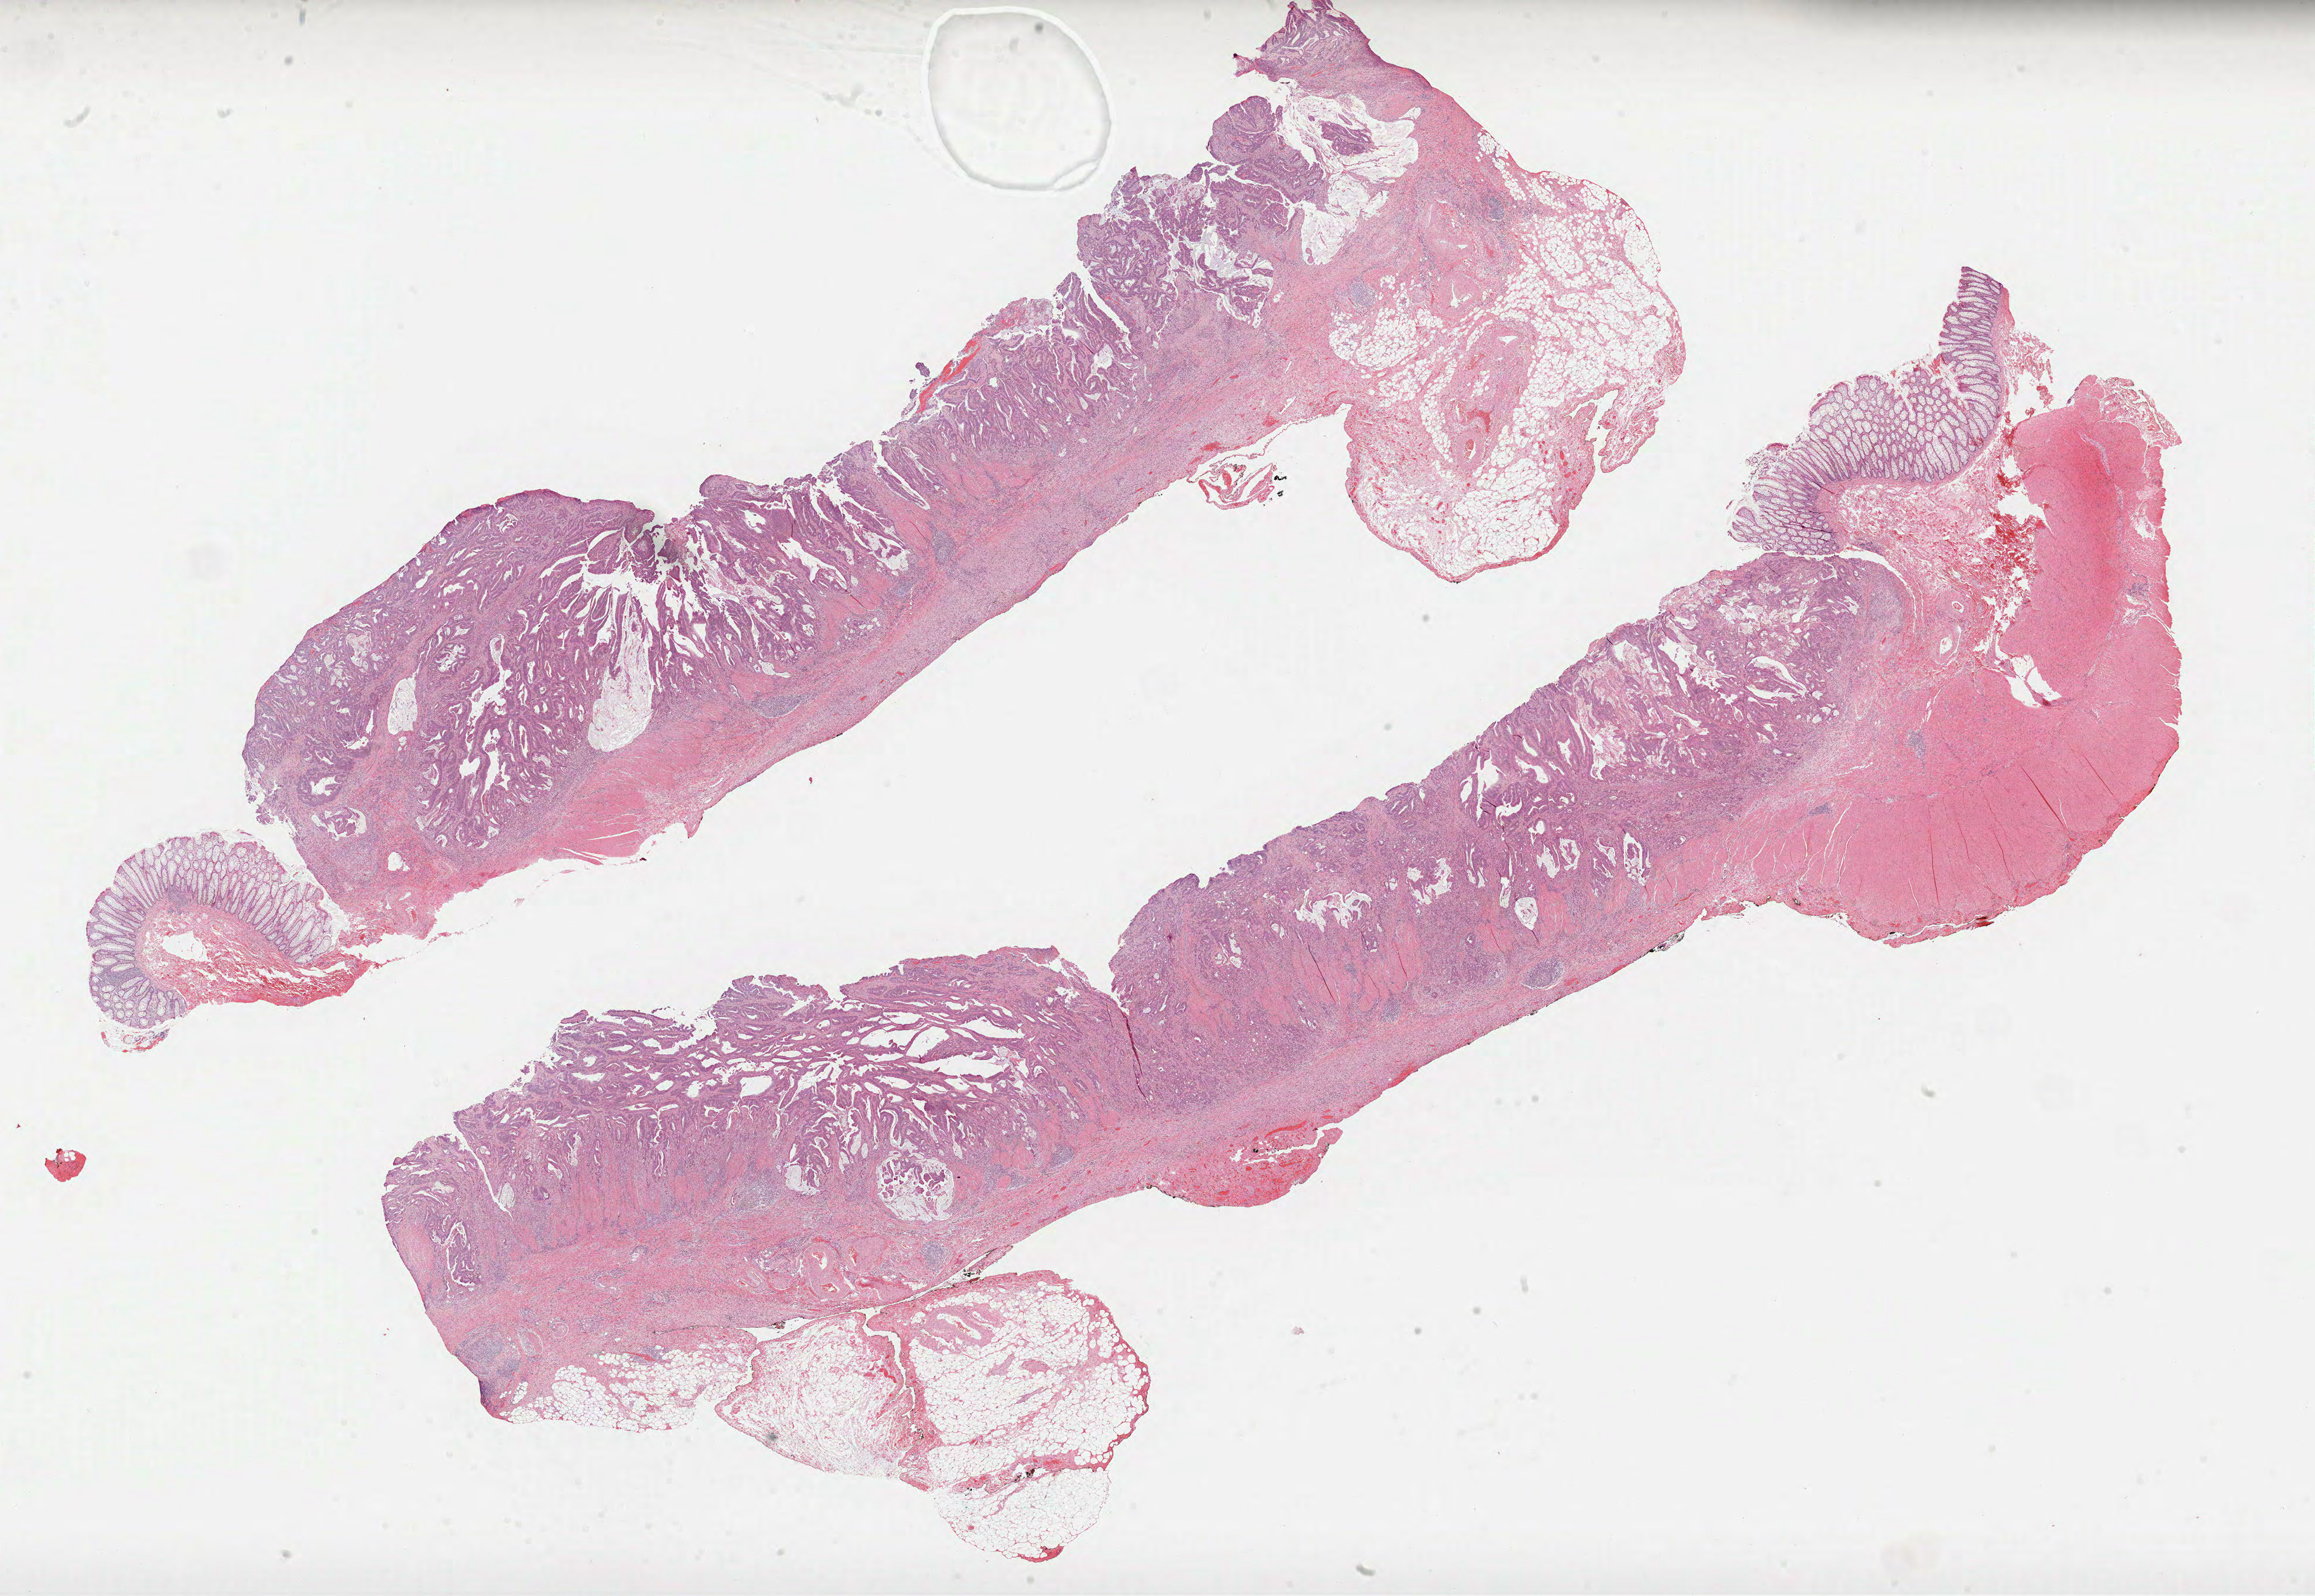
H&E whole-slide image — a low-resolution overview of the entire scanned area, about 31.7 x 21.8 mm (slide scanned at 40x). Formalin-fixed paraffin-embedded (FFPE) diagnostic section. Primary tumour sample from the colon. Female patient; age at initial diagnosis 40 years.
Histologic diagnosis: Adenocarcinoma, NOS.